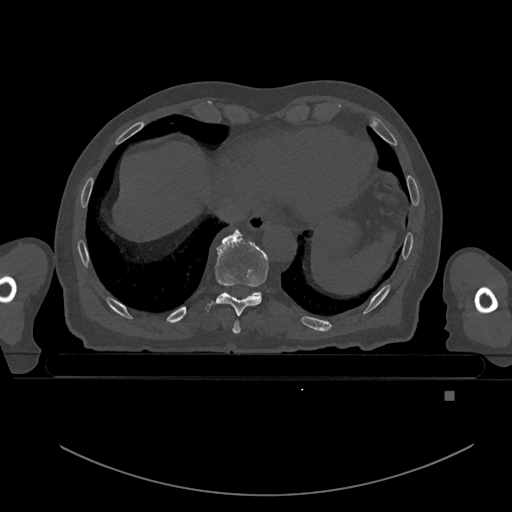
CT including the spine, one axial slice. Slice 139 of 969 in the series (ordered by position). Bone window (W 1800 / L 400 HU). 0.5 mm slice thickness. 512 × 512 image matrix, field of view 456 × 456 mm. Patient: male, 82 years. From the clinical record (not read from this slice): primary cancer: prostate; vertebrae with lytic lesions (as recorded): T11, T9, T8, T2.
Structures marked on this image (semi-automatic segmentation, software-assisted and operator-edited):
- T10 vertebra: box from (x=255, y=292) to (x=260, y=295) px
- T8 vertebra: (x=232, y=320)–(x=241, y=334)
- T9 vertebra: (x=205, y=231)–(x=268, y=316)